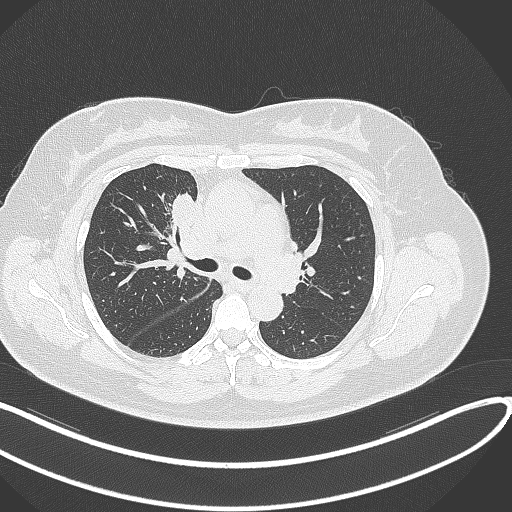
Chest CT, one axial slice; position 175 of 303 along the scan axis; reconstruction kernel B70f; lung window (W 1500 / L -600 HU); 1 mm slice thickness; 512 × 512 image matrix. Female patient, age 46 years. Case-level facts recorded for this patient, not image findings: clinical TNM (as recorded): T2a N1 M0.
Structures marked on this image (rectangle marked by the reading radiologist):
- lung tumour (recorded histology: adenocarcinoma): bounding box (x1, y1, x2, y2) in pixels: (170, 193, 198, 235)